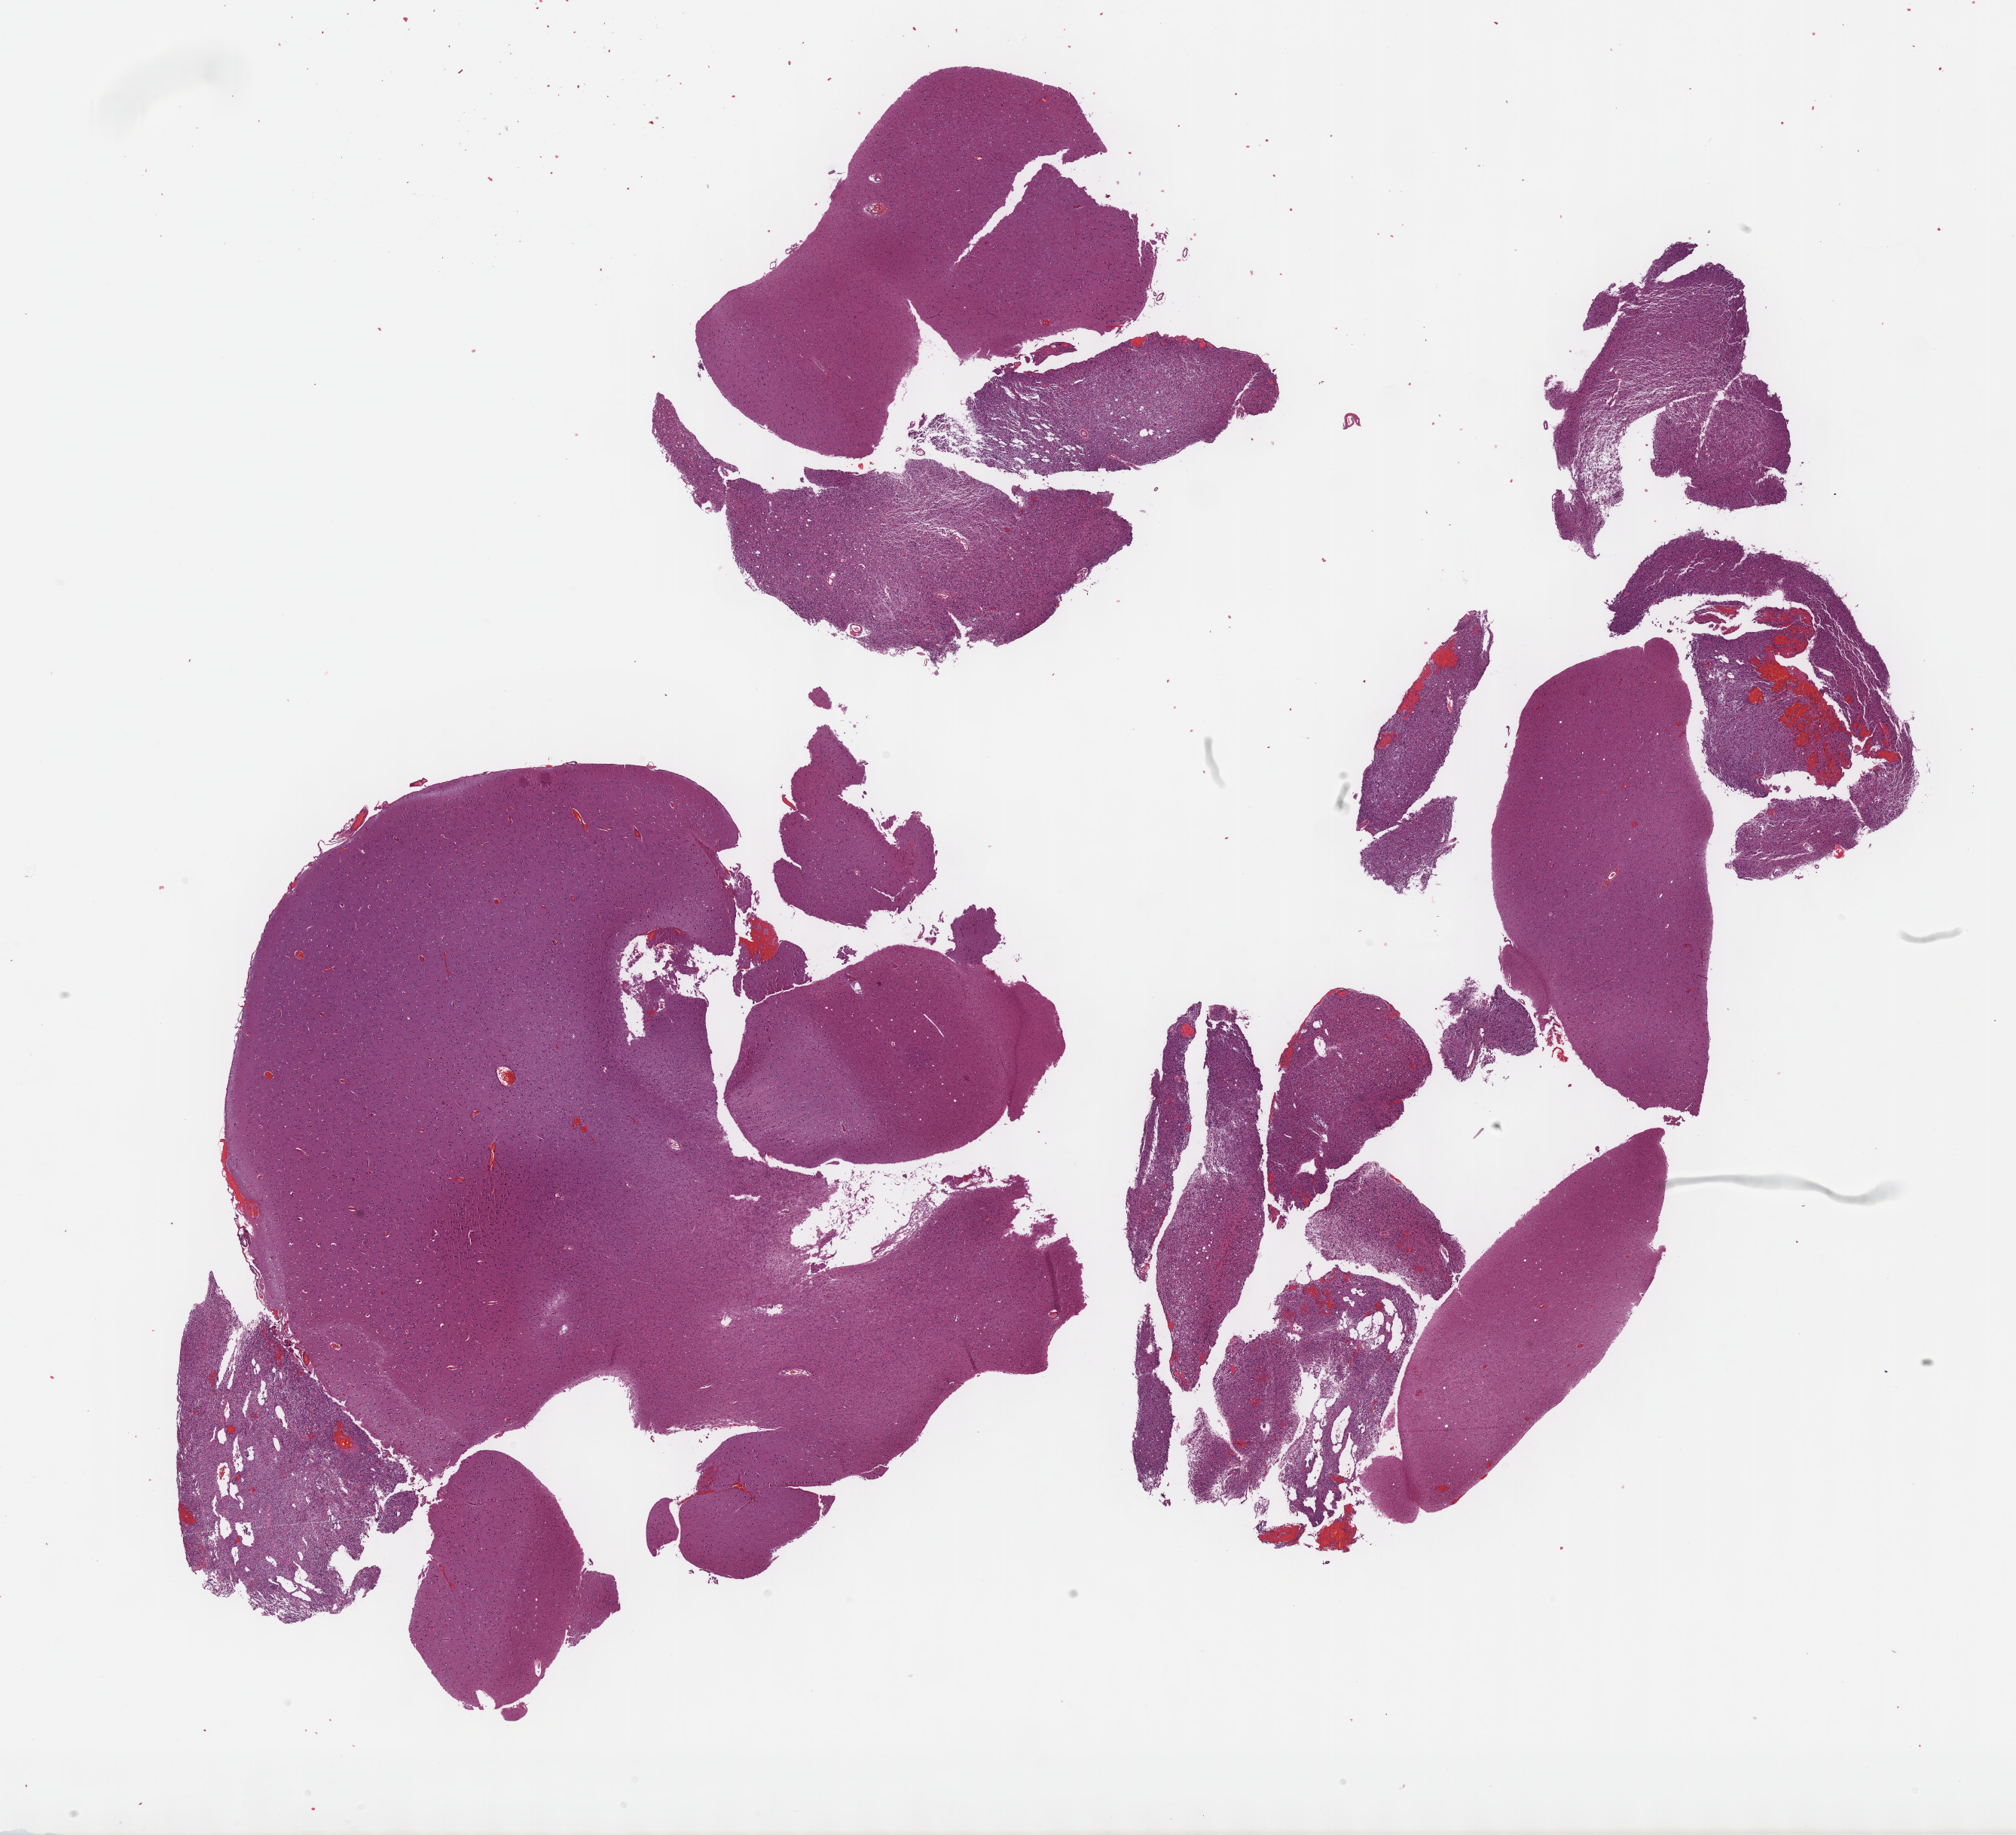
Whole-slide histology image, Hematoxylin and eosin (H&E) stained, whole scanned area (about 21.6 x 19.7 mm) shown as a low-resolution overview. FFPE section. Sample: primary tumour, brain. Female, age 25 years at initial diagnosis. Histologic grade: G2 (moderately differentiated).
Laterality: left. Pathologic diagnosis: Mixed glioma (cerebrum).